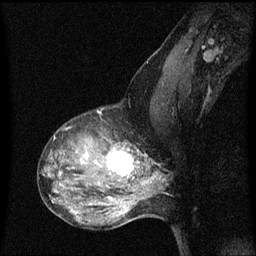
Breast MRI (dynamic contrast-enhanced), one sagittal slice; position 39 of 60 along the scan axis; dynamic contrast-enhanced series, image 2 of 3 at this slice position (ordered by acquisition); 1.5 T; TE 4.2 ms, TR 8 ms; 2 mm slice thickness; 256 × 256 image matrix. Patient: female, 50 years.
Outlined on this slice (semi-automatically segmented with operator editing):
- analysis volume of interest (the breast-tissue region the enhancement analysis was run in; not a lesion): bounding box (x1, y1, x2, y2) in pixels: (91, 132, 141, 189)
- tumour enhancement mask (voxels above the 70 % enhancement threshold inside the analysis volume of interest): (95, 148, 134, 177)